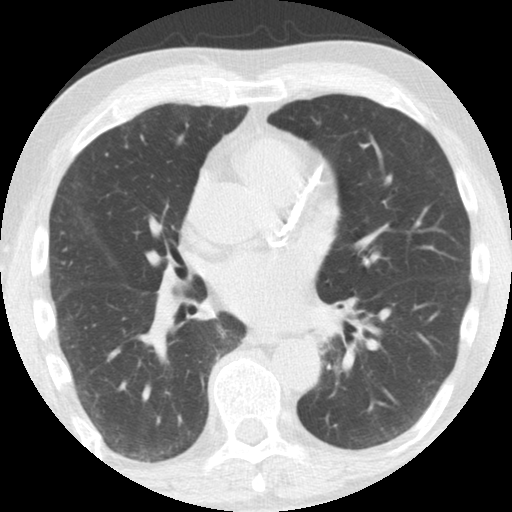
Axial slice from a low-dose chest CT screening exam, third screening round (two years after baseline), lung window (W 1500 / L -600 HU), standard (soft-tissue) reconstruction kernel (STANDARD), 120 kVp, slice 65 of 108 in the series, 512 × 512 image matrix. Male participant, aged 61 years at enrolment. Former smoker at enrolment.
• Expert-annotated lung lesion, bounding box (x1, y1, x2, y2) in pixels: (296, 316, 345, 363).
• Screening reader's record for this exam: no non-calcified nodule ≥4 mm recorded.
• Participant outcome: lung cancer diagnosed 363 days after this screen — squamous cell carcinoma, NOS, left upper lobe, left lower lobe, well differentiated (G1), stage IIB (AJCC 6th edition), 100 mm at pathology.